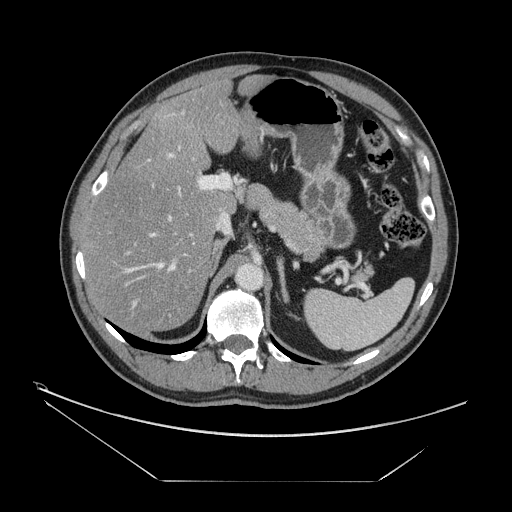
Contrast-enhanced abdominal CT, one axial slice. Slice 93 of 161 in the series (ordered by position). Reconstruction kernel STANDARD. 120 kVp. Intravenous contrast given. Soft-tissue window (W 400 / L 40 HU). 512 × 512 image matrix, field of view 440 × 440 mm. Male patient, age 65 years. From the clinical record (not read from this slice): diagnosis: colorectal cancer liver metastases, imaged before liver resection; multiple liver metastases: yes; largest metastasis: 4.2 cm; chemotherapy before resection: yes.
Annotated regions visible in this slice (expert manual segmentation):
- hepatic veins: bounding box [x1, y1, x2, y2] px = [124, 183, 181, 307]
- liver: [85, 79, 270, 330]
- planned liver remnant (the part of the liver to remain after resection): [85, 79, 270, 330]
- portal vein (with intrahepatic branches): [124, 153, 230, 317]